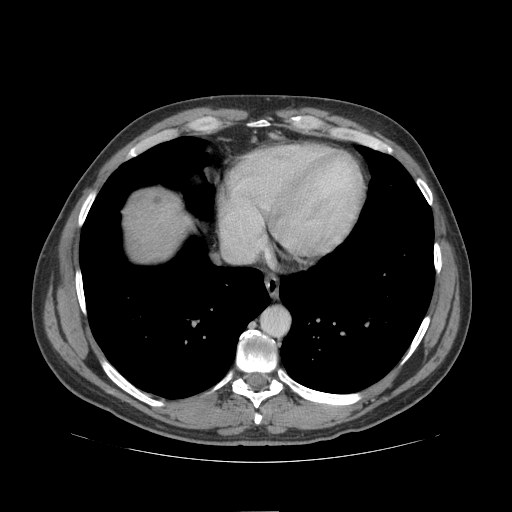
Contrast-enhanced abdominal CT (liver protocol), one axial slice; position 97 of 109 along the scan axis; reconstruction kernel STANDARD; soft-tissue window (W 400 / L 40 HU); 512 × 512 image matrix, field of view 420 × 420 mm. Case-level facts recorded for this patient, not image findings: diagnosis: hepatocellular carcinoma (patient treated with transarterial chemoembolisation; whether this scan precedes or follows treatment is not stated here); TNM stage (as recorded): Stage-IIIB; Child-Pugh class: A.
Outlined on this slice (semi-automatic segmentation, software-assisted and operator-edited):
- liver parenchyma outside the tumour (the mass and vessels are separate outlines, so this box may not span the whole liver): bounding box <124,190,188,260> (left, top, right, bottom; pixels)
- mass: <134,192,170,208>